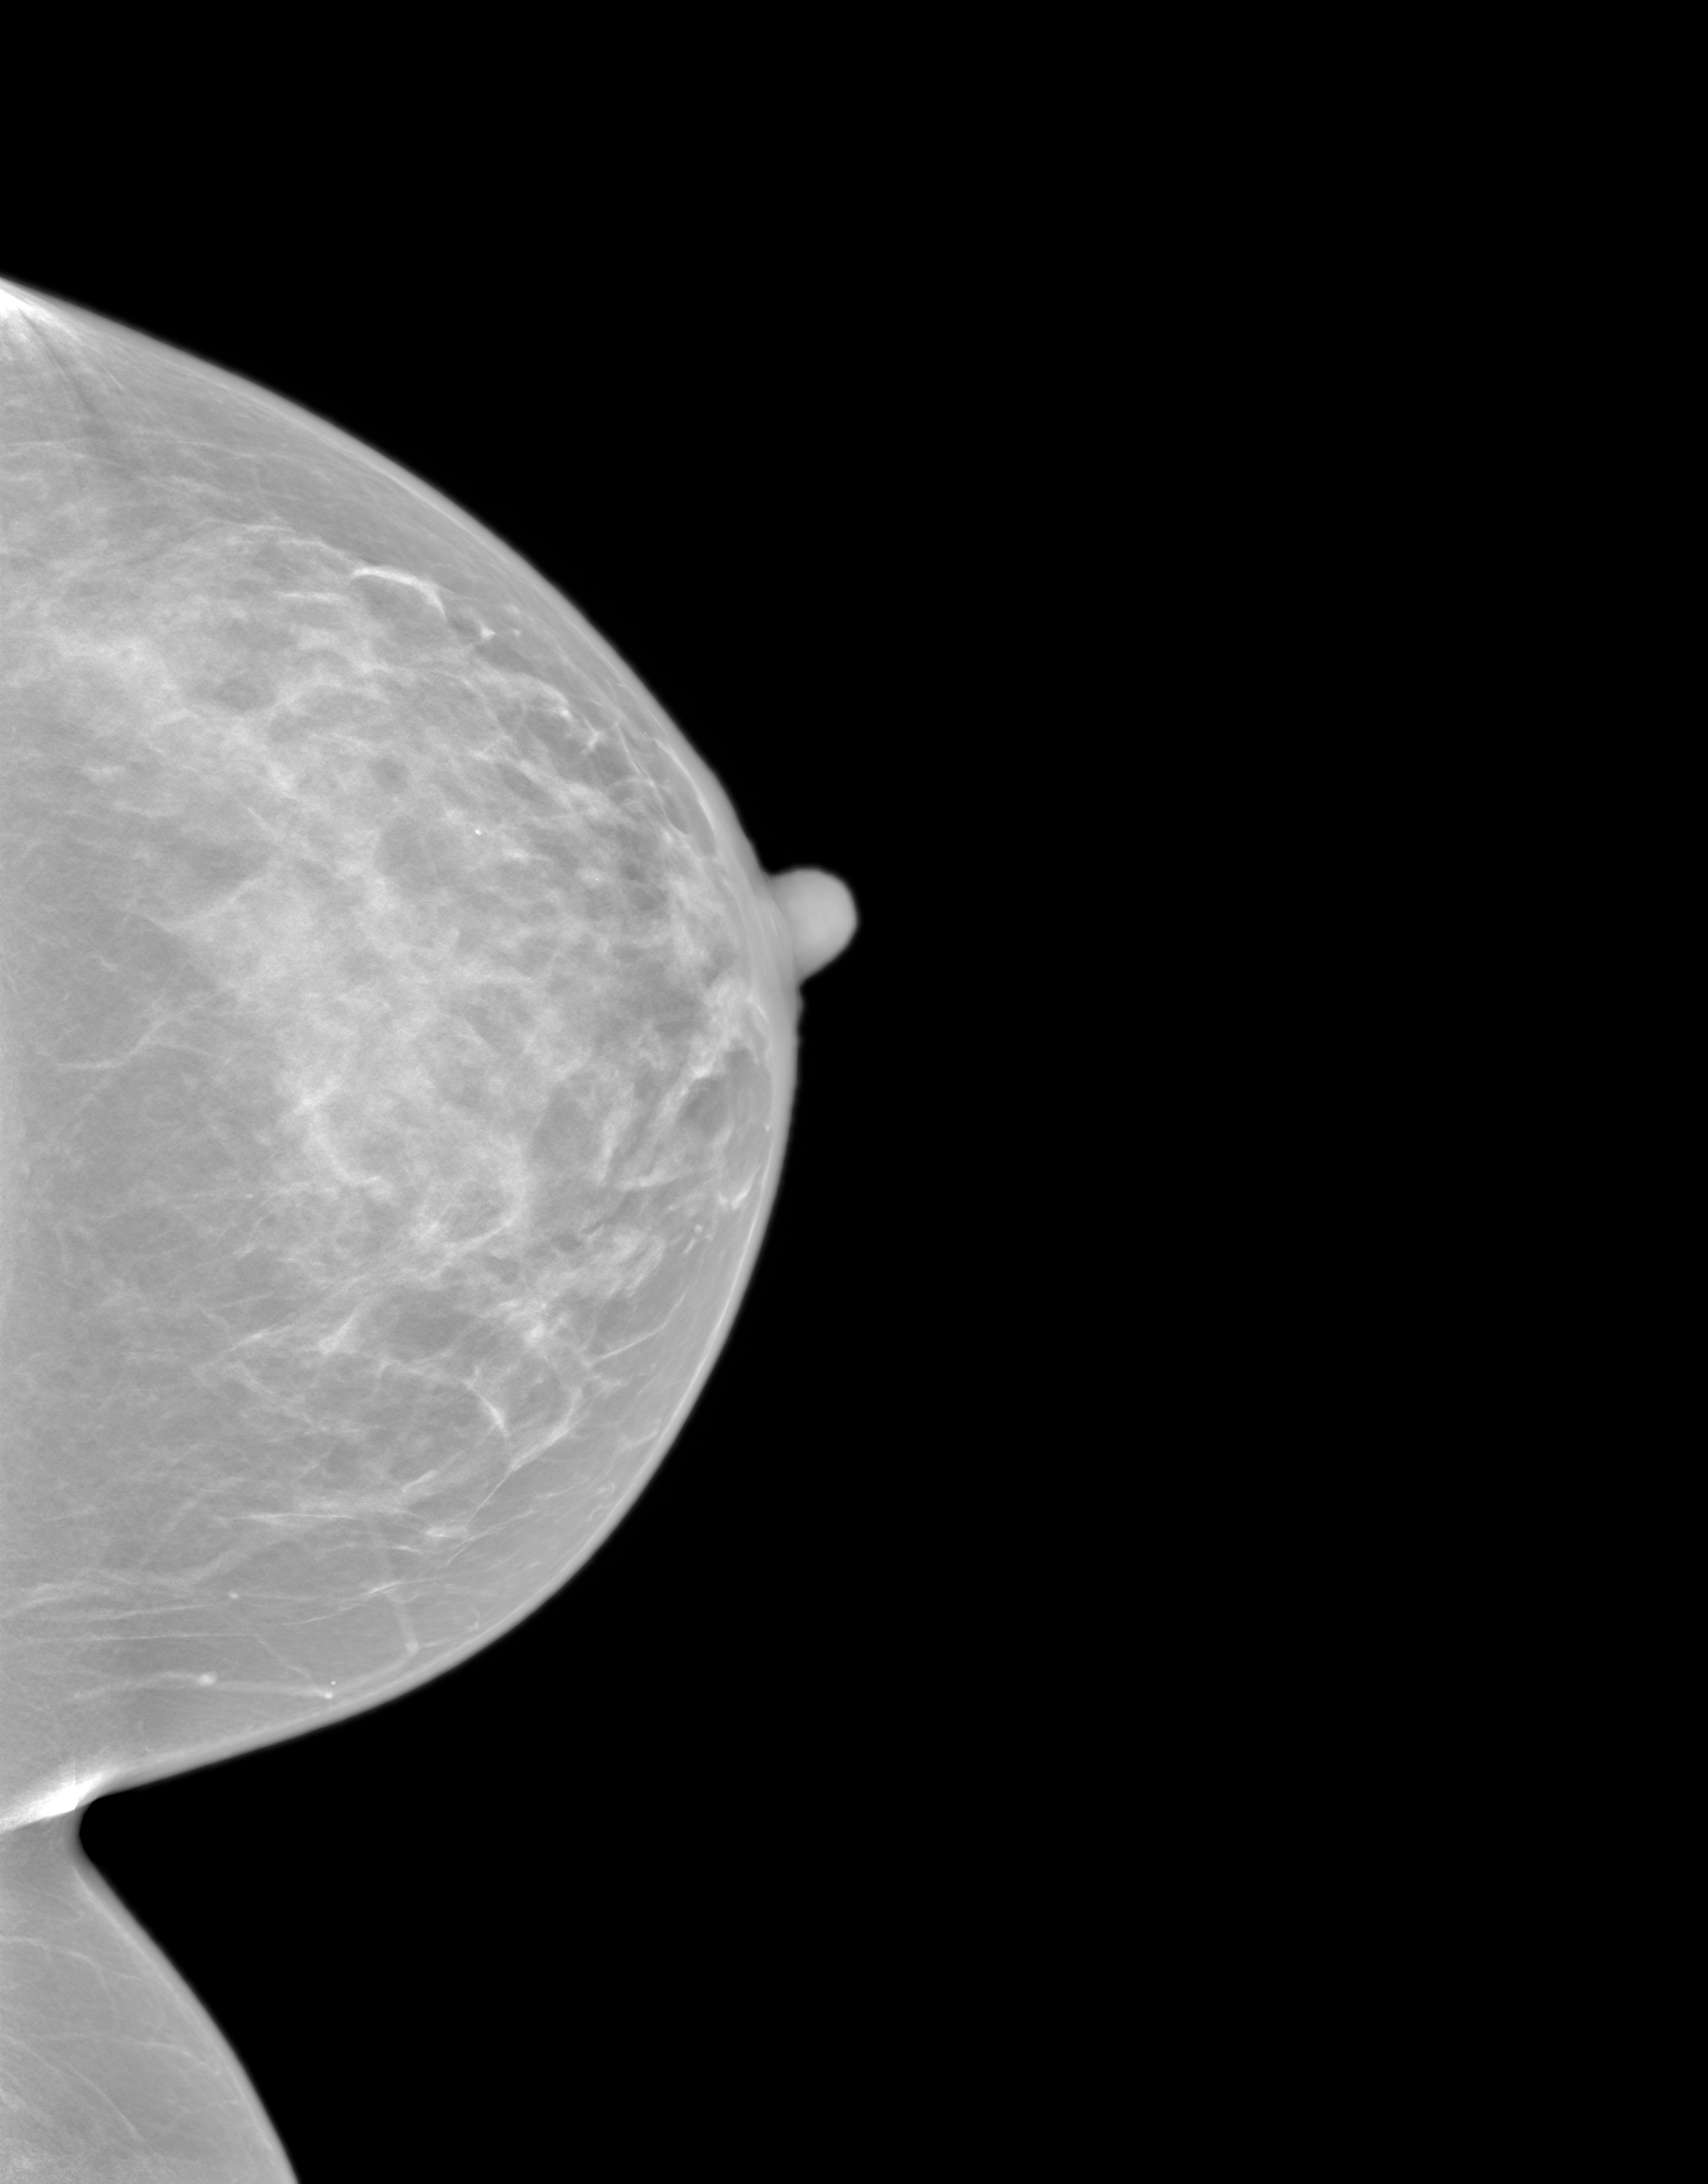
Annual screening mammography examination. Patient aged 50 years (female).
Image type: synthesized 2-D view from tomosynthesis. Breast: left. Projection: CC view.